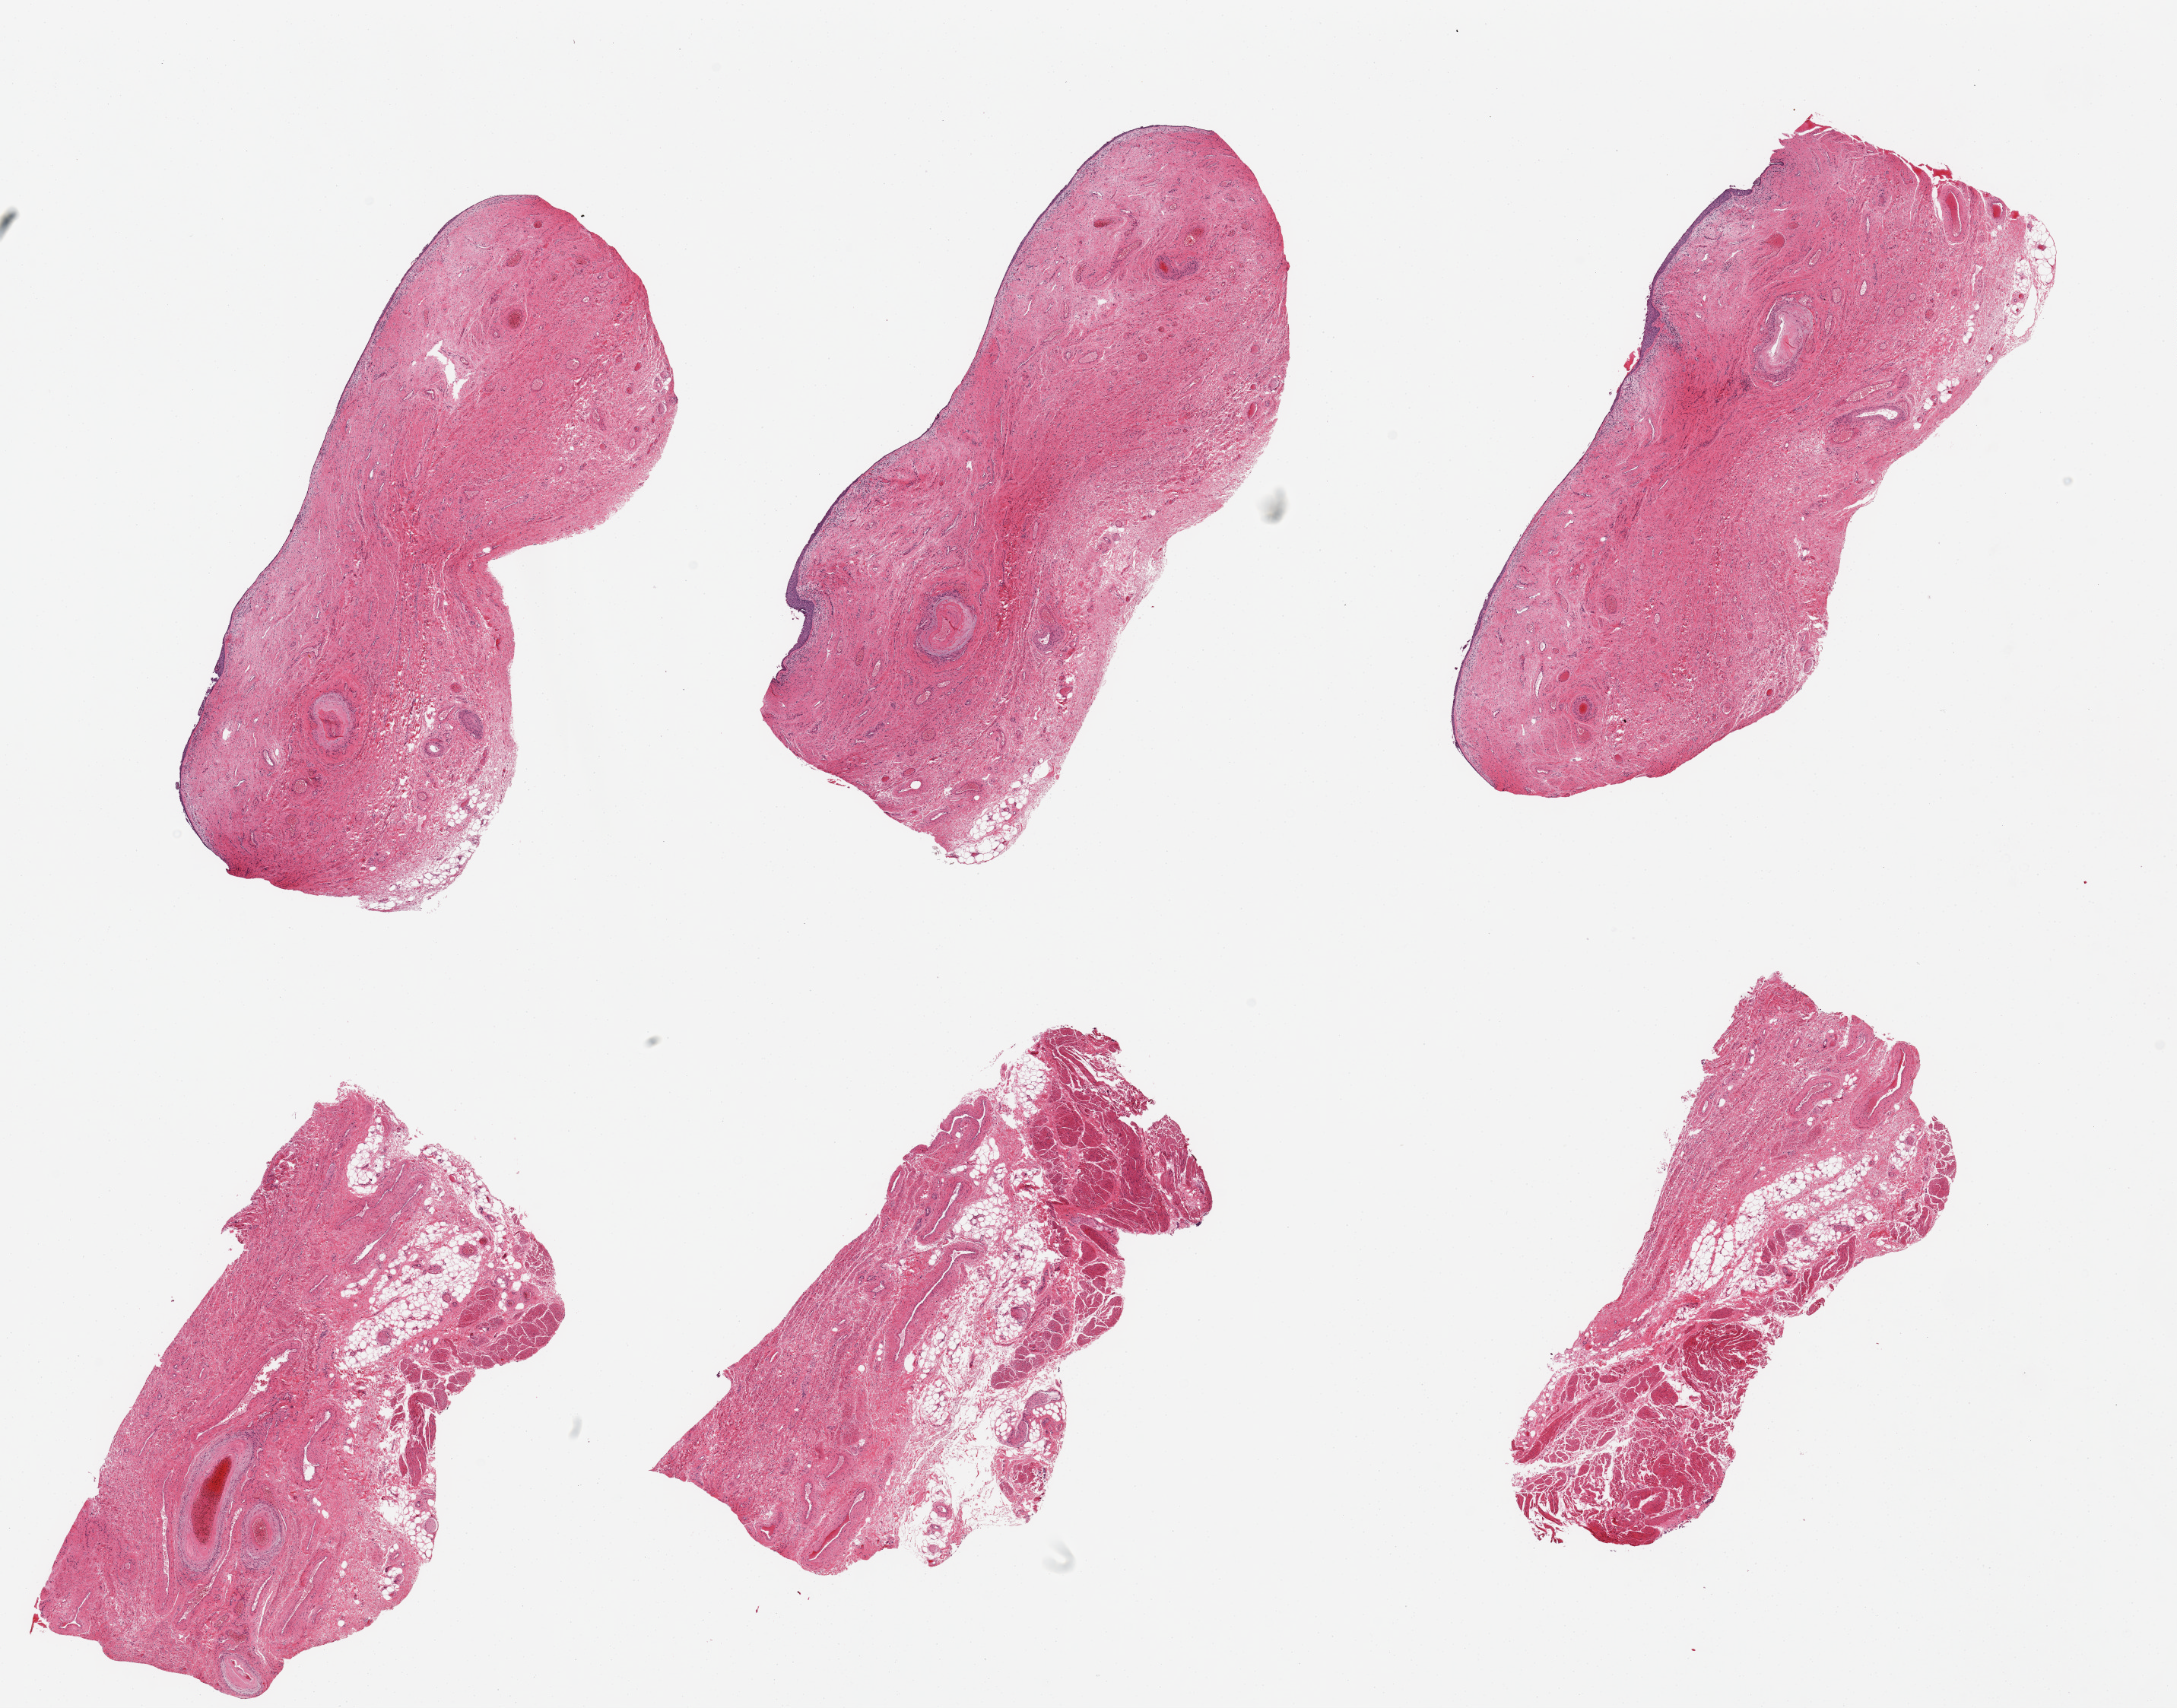
H&E whole-slide image, brightfield, whole scanned area (about 22.6 x 17.8 mm) shown as a low-resolution overview. PAXgene-fixed, paraffin-embedded tissue. Sampled site (target tissue): vagina. Donor tissue sample. Donor sex: female.
Review note (as recorded): 6 pieces; 3 with largely sloughed mucosa, 3 with outer wall and 30% fat.